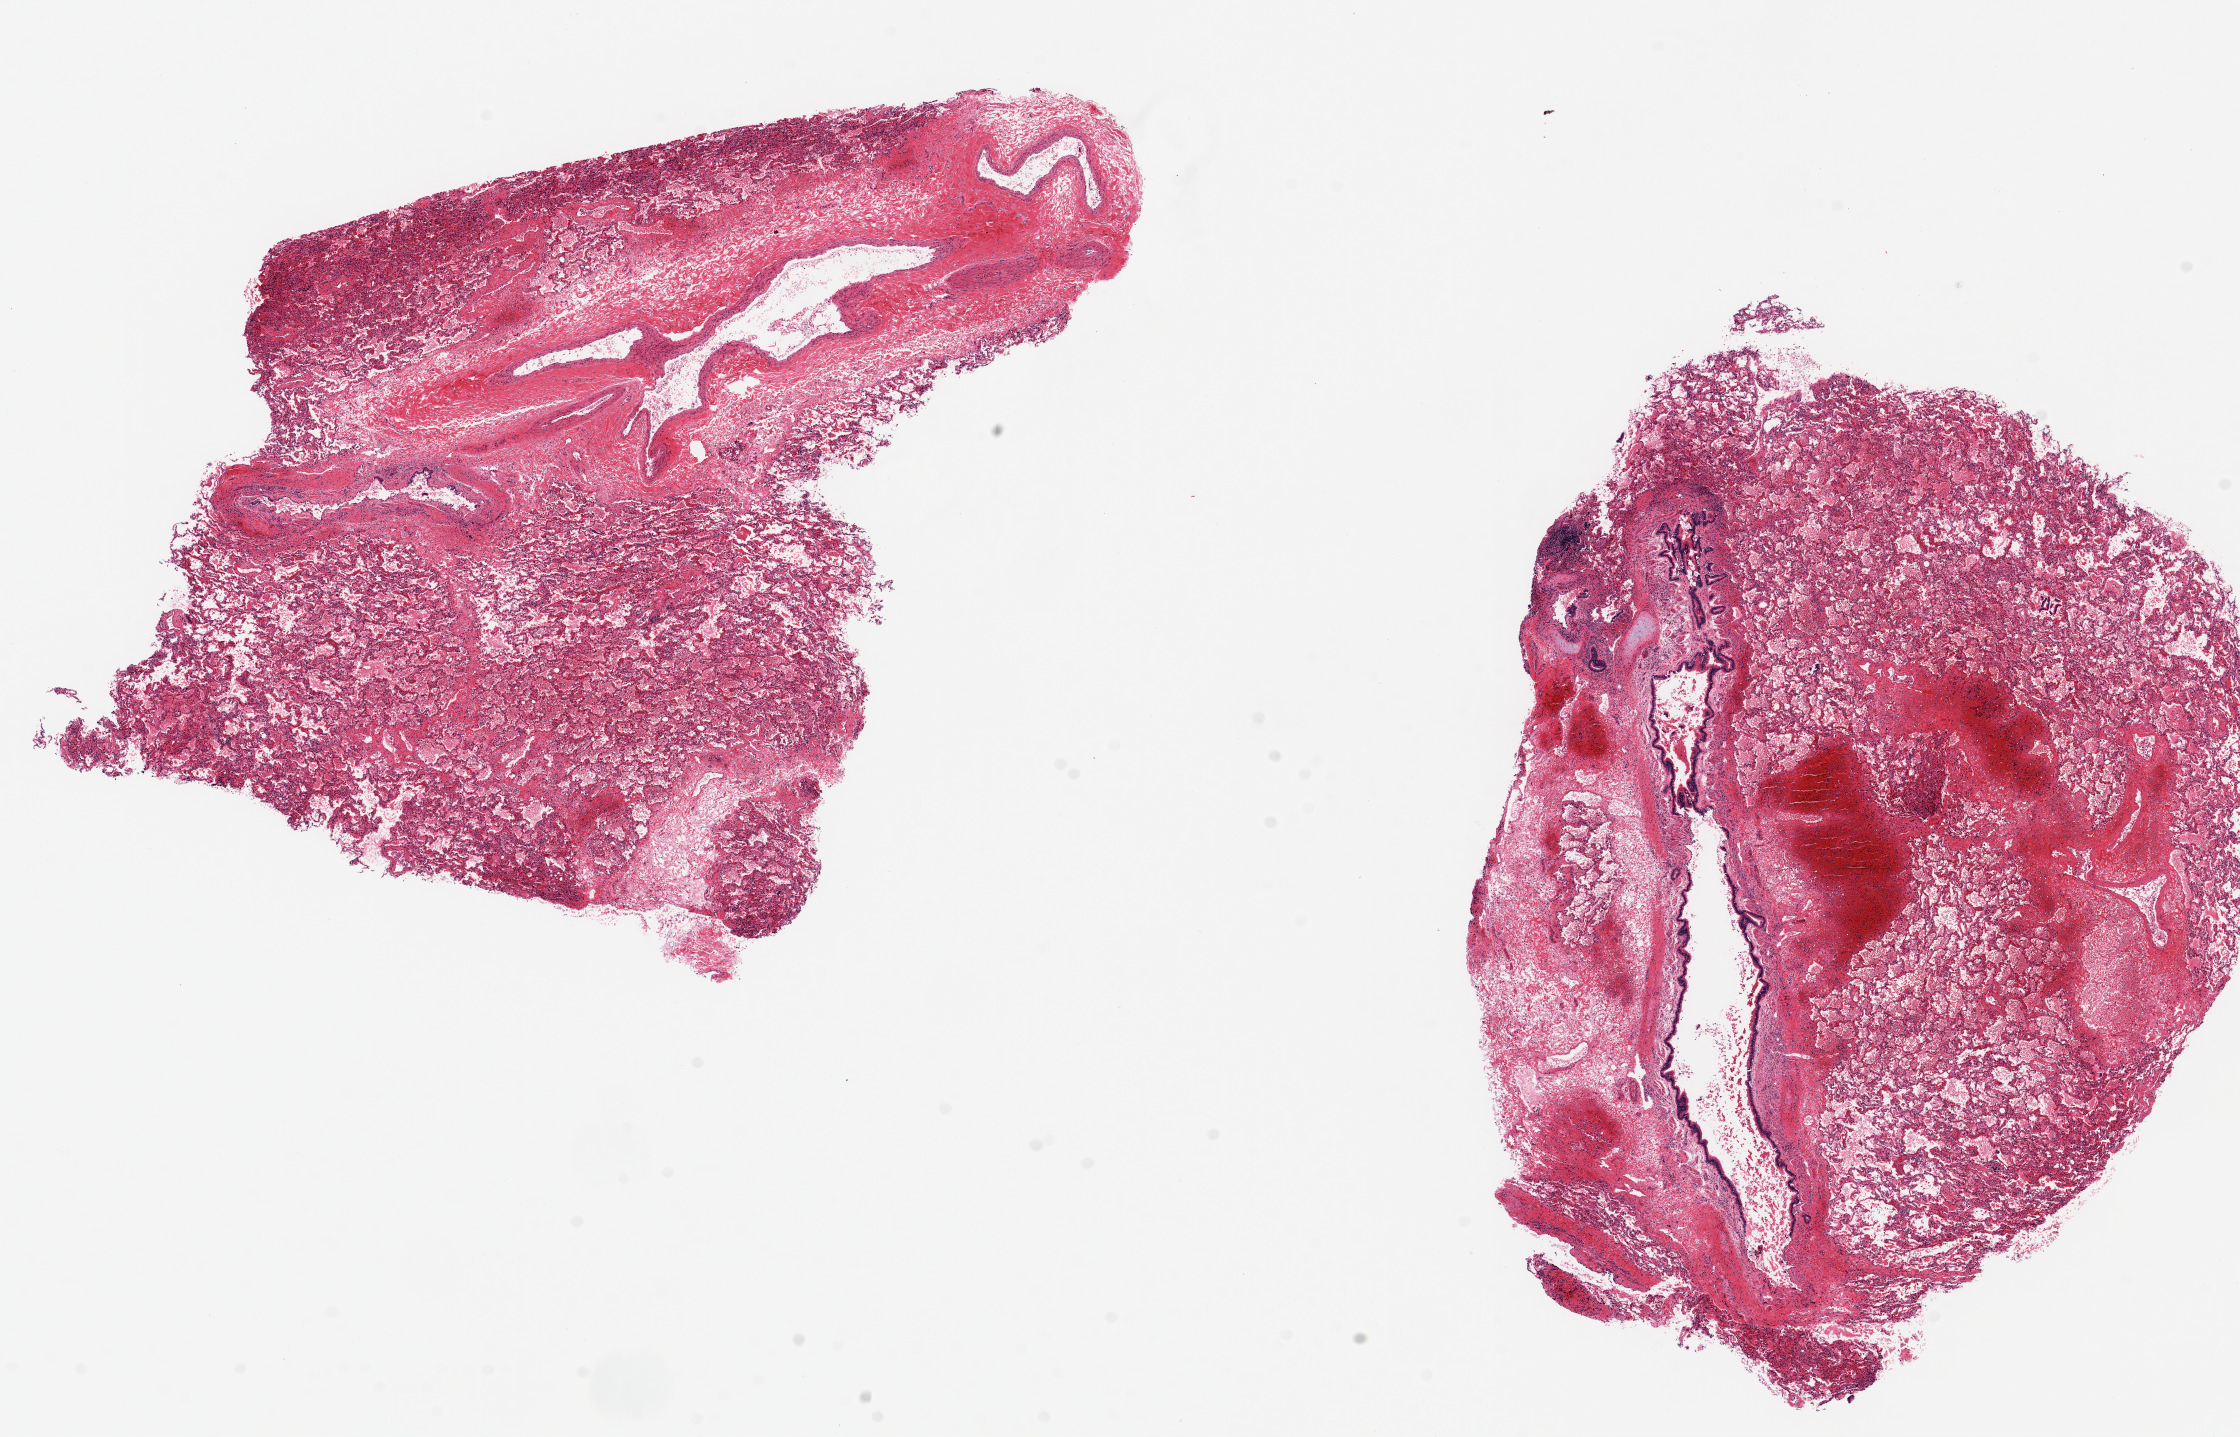
Digitized haematoxylin and eosin-stained section — a low-resolution overview of the entire scanned area, about 17.7 x 11.4 mm; PAXgene-fixed paraffin-embedded (PFPE) section; target tissue: lung; tissue donor sample.
Review note (as recorded): 2 pieces ~7x6mm, both with ~20% vessel/bronchus; Prominent parenchymal hemorrhage in both, probably trauma-related.